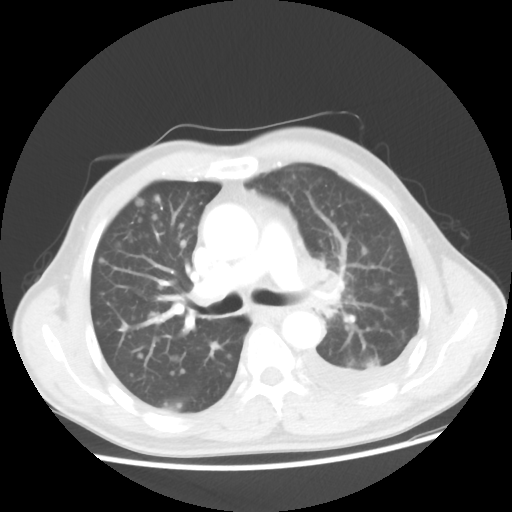
Chest CT, one axial slice; slice 29 of 48 in the series (ordered by position); reconstruction kernel STANDARD; 100 kVp; lung window (W 1500 / L -600 HU); 5 mm slice thickness; 512 × 512 image matrix, field of view 362 × 362 mm. Patient: male, 55 years. Case-level facts recorded for this patient, not image findings: clinical TNM (as recorded): T2 N3 M1a.
Structures marked on this image (bounding box drawn by a radiologist):
- lung tumour (recorded histology: squamous cell carcinoma): bounding box [x1, y1, x2, y2] px = [320, 253, 354, 324]